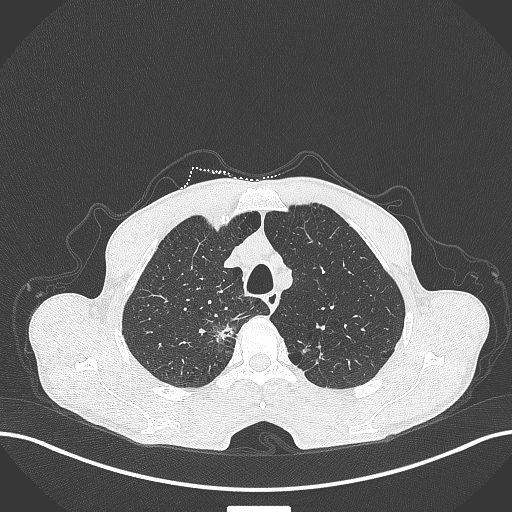
Chest CT, one axial slice; 120 kVp; lung window (W 1500 / L -600 HU); 512 × 512 image matrix. Male patient, age 70 years. From the clinical record (not read from this slice): clinical TNM (as recorded): T1a N0 M0.
Annotated regions visible in this slice (bounding box drawn by a radiologist):
- lung tumour (recorded histology: adenocarcinoma): bounding box (x1, y1, x2, y2) in pixels: (213, 320, 236, 347)